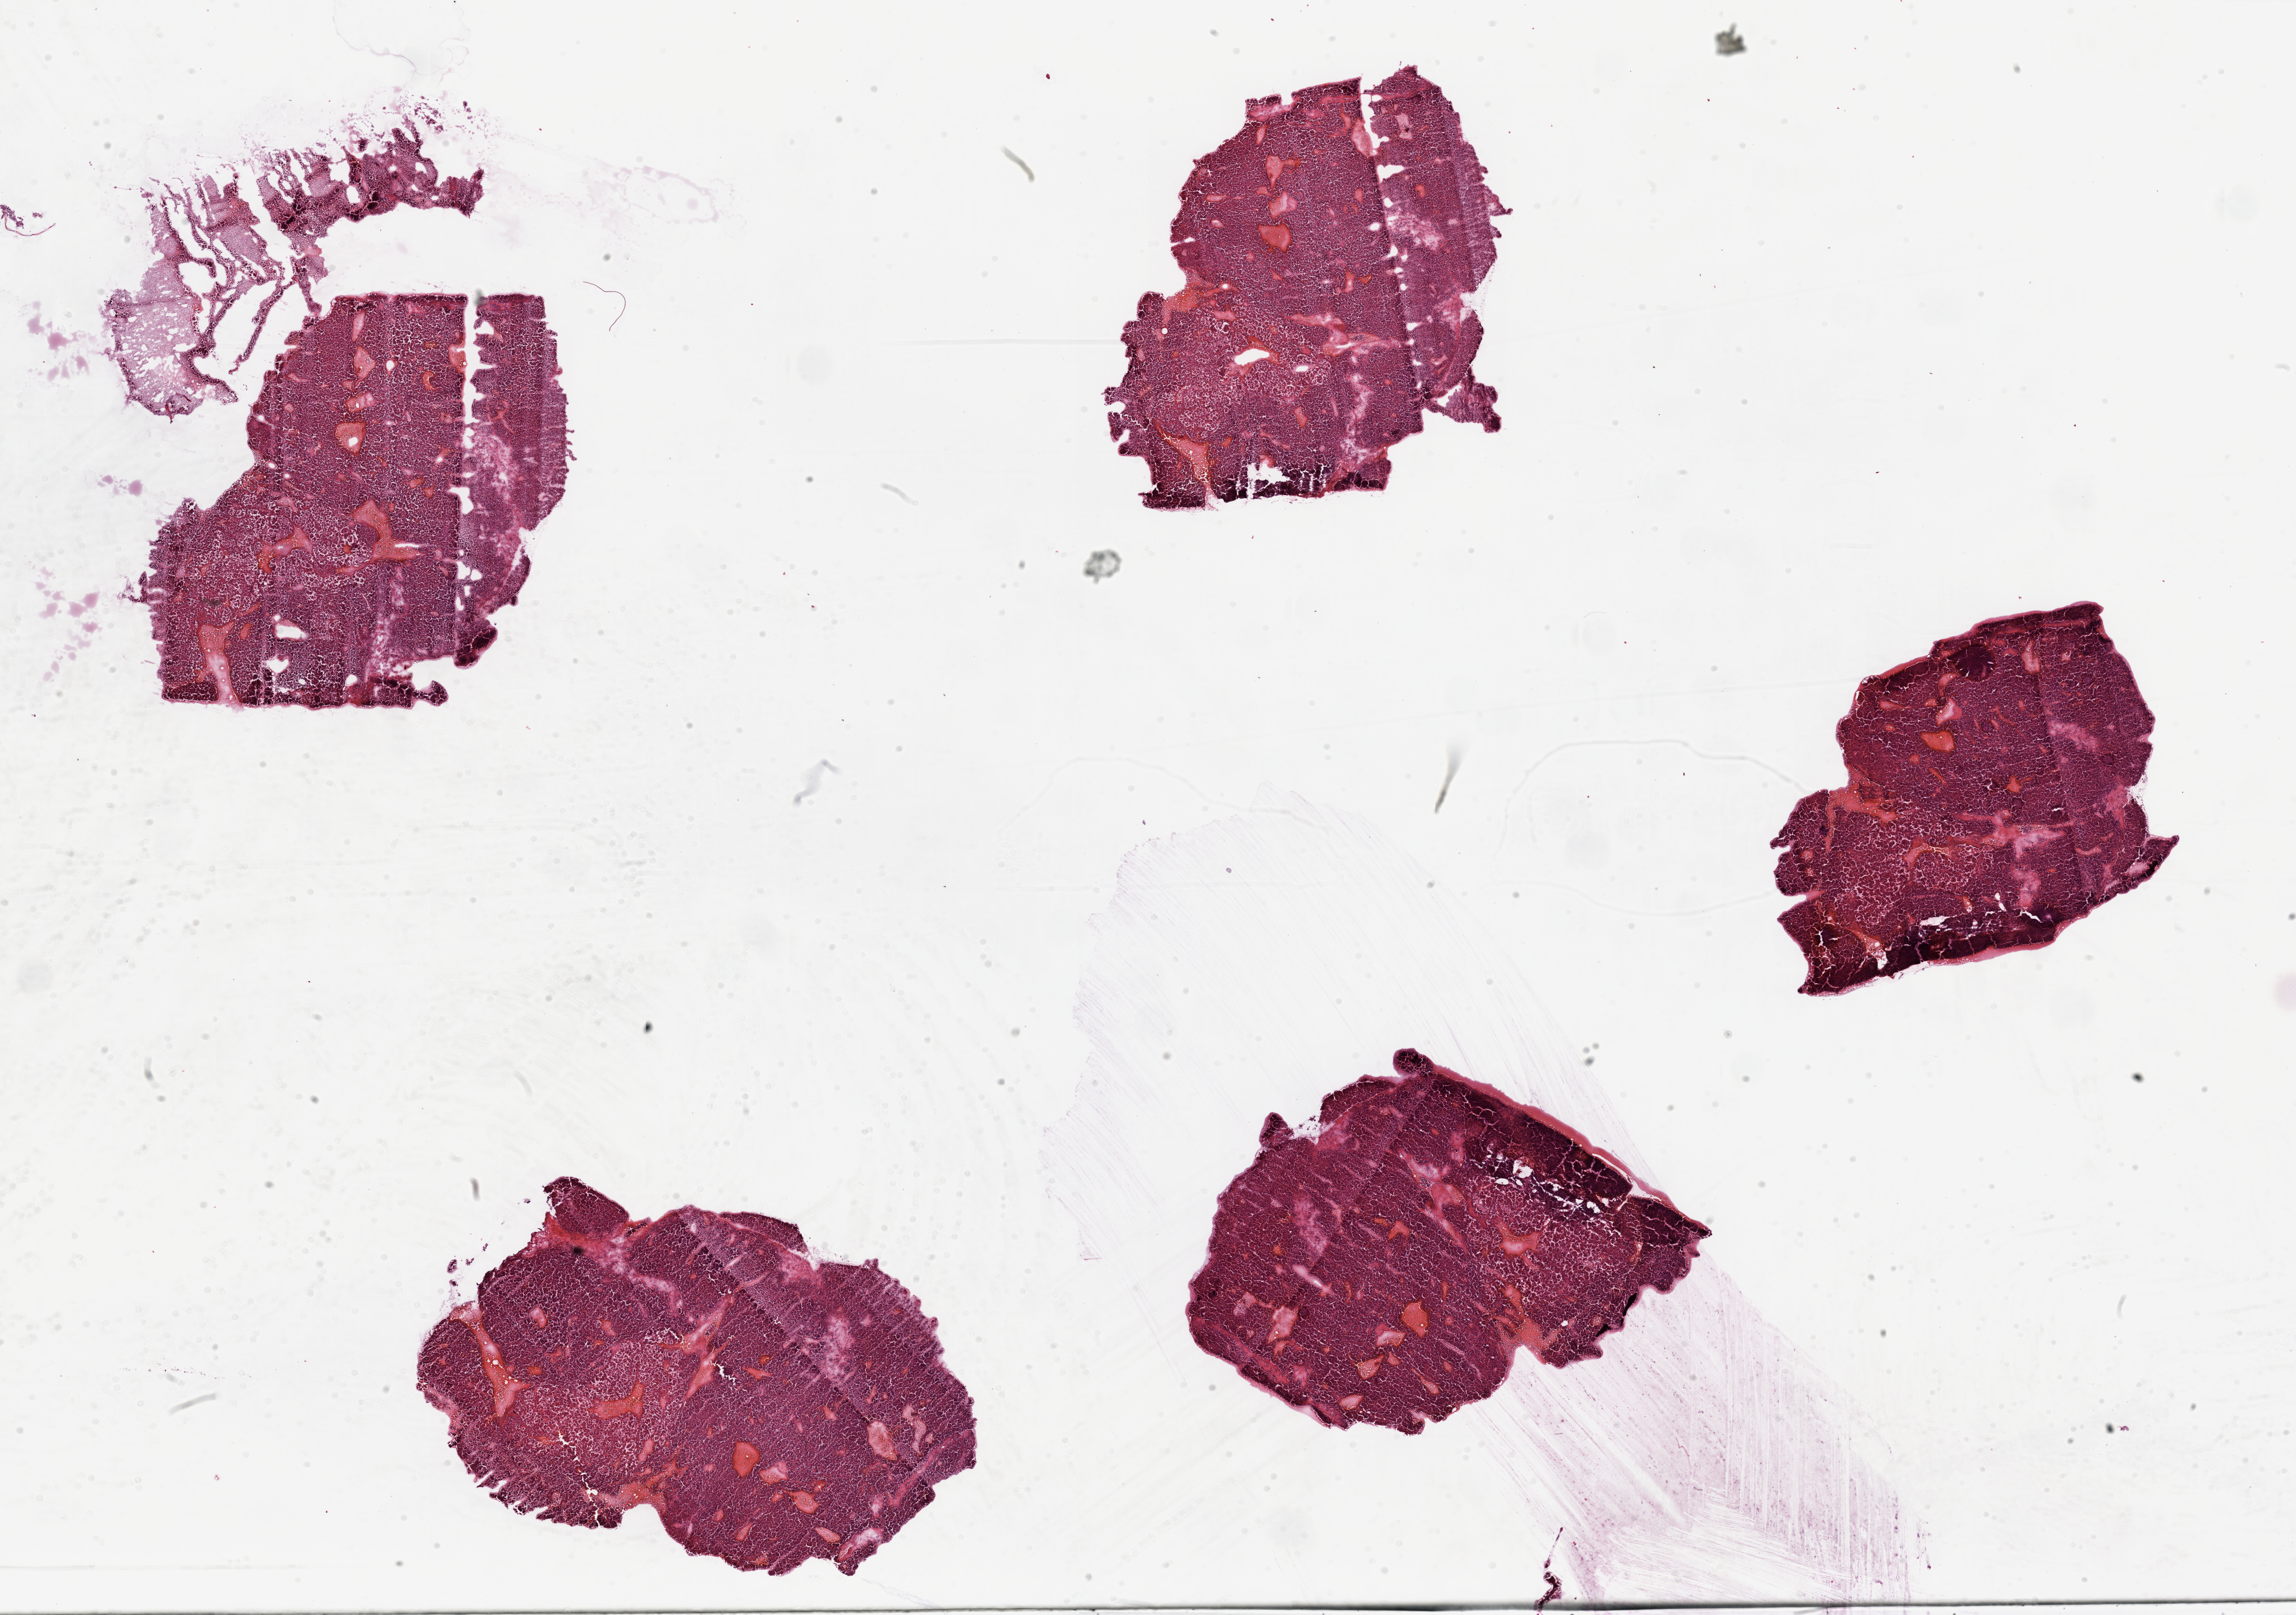
H&E whole-slide image — shown as a low-resolution overview of the whole scanned area (about 31.5 x 22.2 mm); tumour tissue sample, sampled site: kidney. Male, 67 y/o. Histologic grade: G2 (moderately differentiated). Pathologist review of this section (percent, as recorded): tumour nuclei 80%, necrosis 10%.
Primary tumour site (as recorded): middle. Diagnosis: Renal cell carcinoma, NOS. AJCC pathologic stage: III.